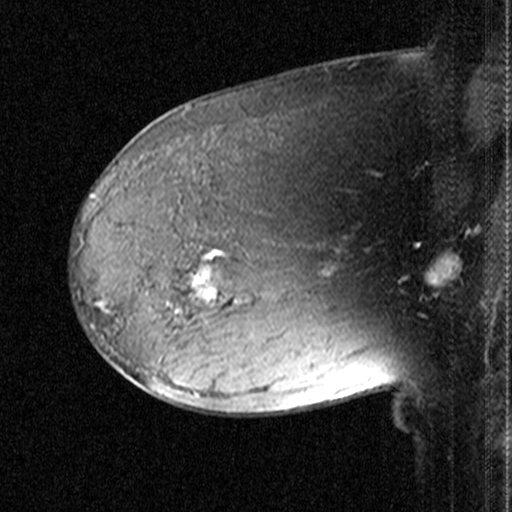
Breast MRI (dynamic contrast-enhanced), one sagittal slice; slice 28 of 44 in the series (ordered by position); dynamic contrast-enhanced study with each time point stored as its own series, time point 2 of 3 at this slice position (early post-contrast, ordered by acquisition time); 1.5 T; TE 4.5 ms, TR 11 ms; 512 × 512 image matrix, field of view 200 × 200 mm. Female patient, age 38 years. Case-level facts recorded for this patient, not image findings: setting: breast cancer imaged before/during neoadjuvant chemotherapy; receptor status: HR-positive, HER2-negative.
Outlined on this slice (semi-automatic segmentation, software-assisted and operator-edited):
- analysis volume of interest (the breast-tissue region the enhancement analysis was run in; not a lesion): bounding box (x1, y1, x2, y2) in pixels: (170, 232, 259, 331)
- tumour enhancement mask (voxels above the 90 % enhancement threshold inside the analysis volume of interest): (191, 251, 223, 303)